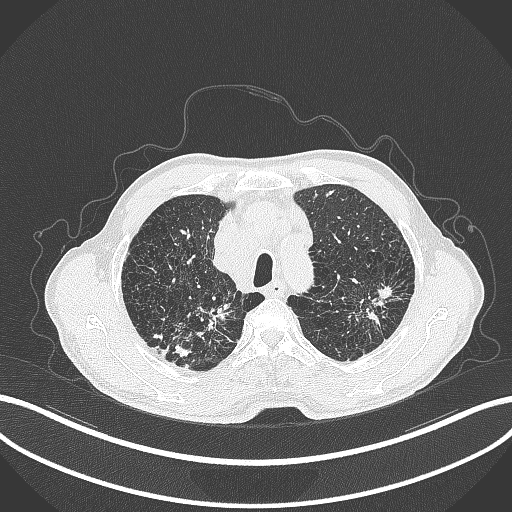
Chest CT, one axial slice. Position 361 of 463 along the scan axis. Reconstruction kernel B70f. Lung window (W 1500 / L -600 HU). 1 mm slice thickness. 512 × 512 image matrix. Patient: male, 74 years. Case-level facts recorded for this patient, not image findings: clinical TNM (as recorded): T2a N1 M0.
Annotated regions visible in this slice (rectangle marked by the reading radiologist):
- lung tumour (recorded histology: adenocarcinoma): bounding box (x1, y1, x2, y2) in pixels: (350, 280, 395, 332)